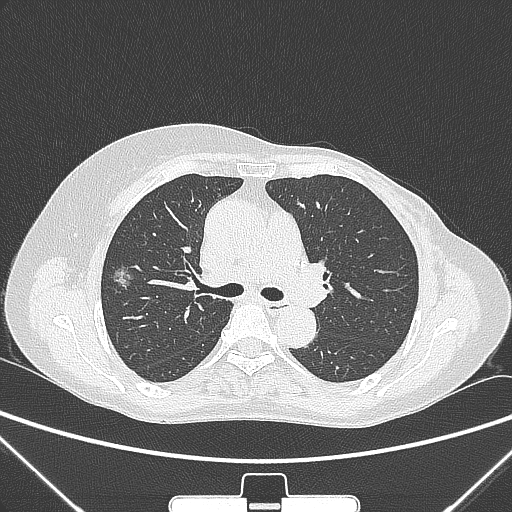
Chest CT, one axial slice; position 160 of 265 along the scan axis; lung window (W 1500 / L -600 HU); 1 mm slice thickness; 512 × 512 image matrix. Patient: female, 64 years. From the clinical record (not read from this slice): clinical TNM (as recorded): T1c N0 M0.
Outlined on this slice (rectangle marked by the reading radiologist):
- lung tumour (recorded histology: adenocarcinoma): box from (x=109, y=258) to (x=137, y=294) px